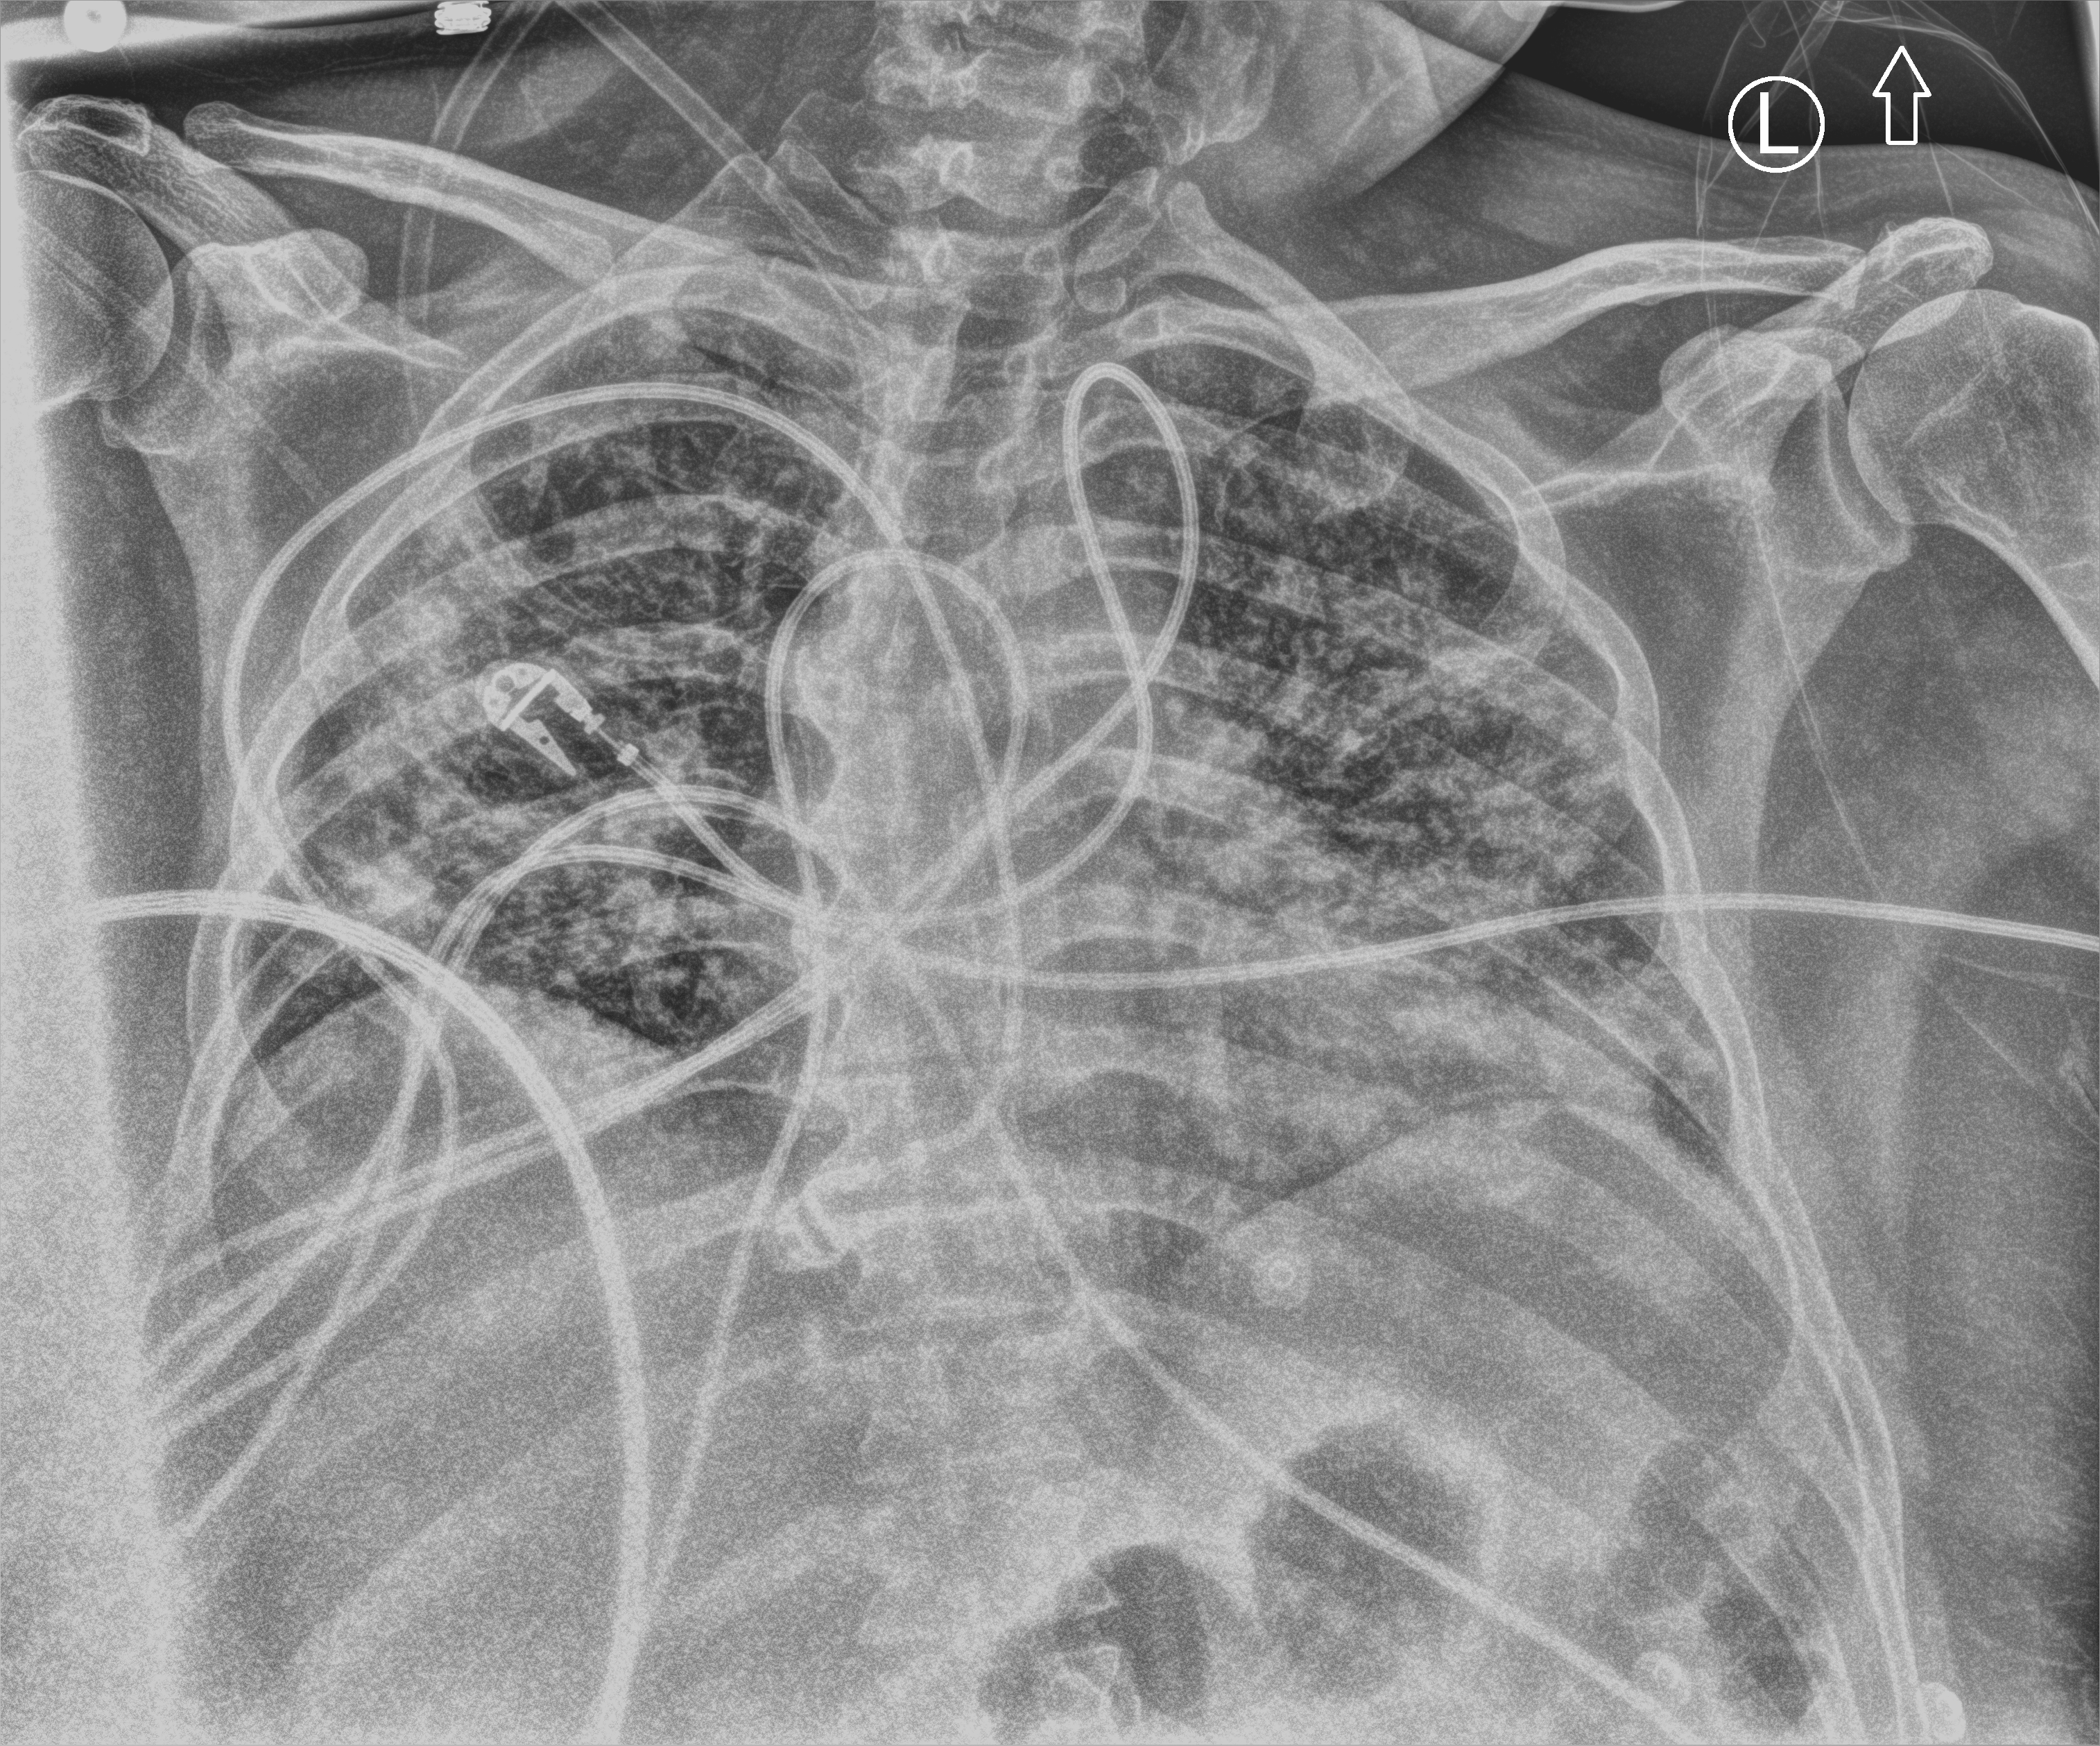
Portable chest radiograph; anteroposterior (AP) projection. Male patient hospitalised with COVID-19, age 18–59 years.
From the hospital-stay record, not from the radiograph (when in the stay this image was taken is not recorded):
- mechanically ventilated during this hospital stay: yes